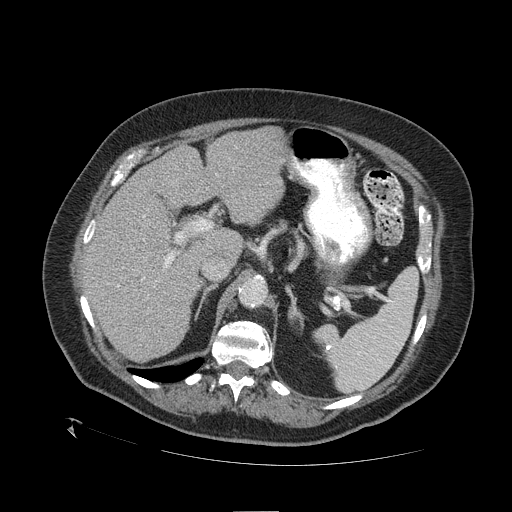
Contrast-enhanced abdominal CT (liver protocol), one axial slice. Slice 71 of 109 in the series (ordered by position). 120 kVp. One of 2 acquisitions stored at this slice position. Soft-tissue window (W 400 / L 40 HU). 512 × 512 image matrix, field of view 460 × 460 mm. From the clinical record (not read from this slice): diagnosis: hepatocellular carcinoma (patient treated with transarterial chemoembolisation; whether this scan precedes or follows treatment is not stated here); TNM stage (as recorded): Stage-I; Child-Pugh class: A; tumour differentiation: no biopsy; tumour nodularity: uninodular.
Structures marked on this image (semi-automatic segmentation, software-assisted and operator-edited):
- liver parenchyma outside the tumour (the mass and vessels are separate outlines, so this box may not span the whole liver): bounding box (x1, y1, x2, y2) in pixels: (82, 128, 286, 361)
- liver vessels: (92, 216, 174, 287)